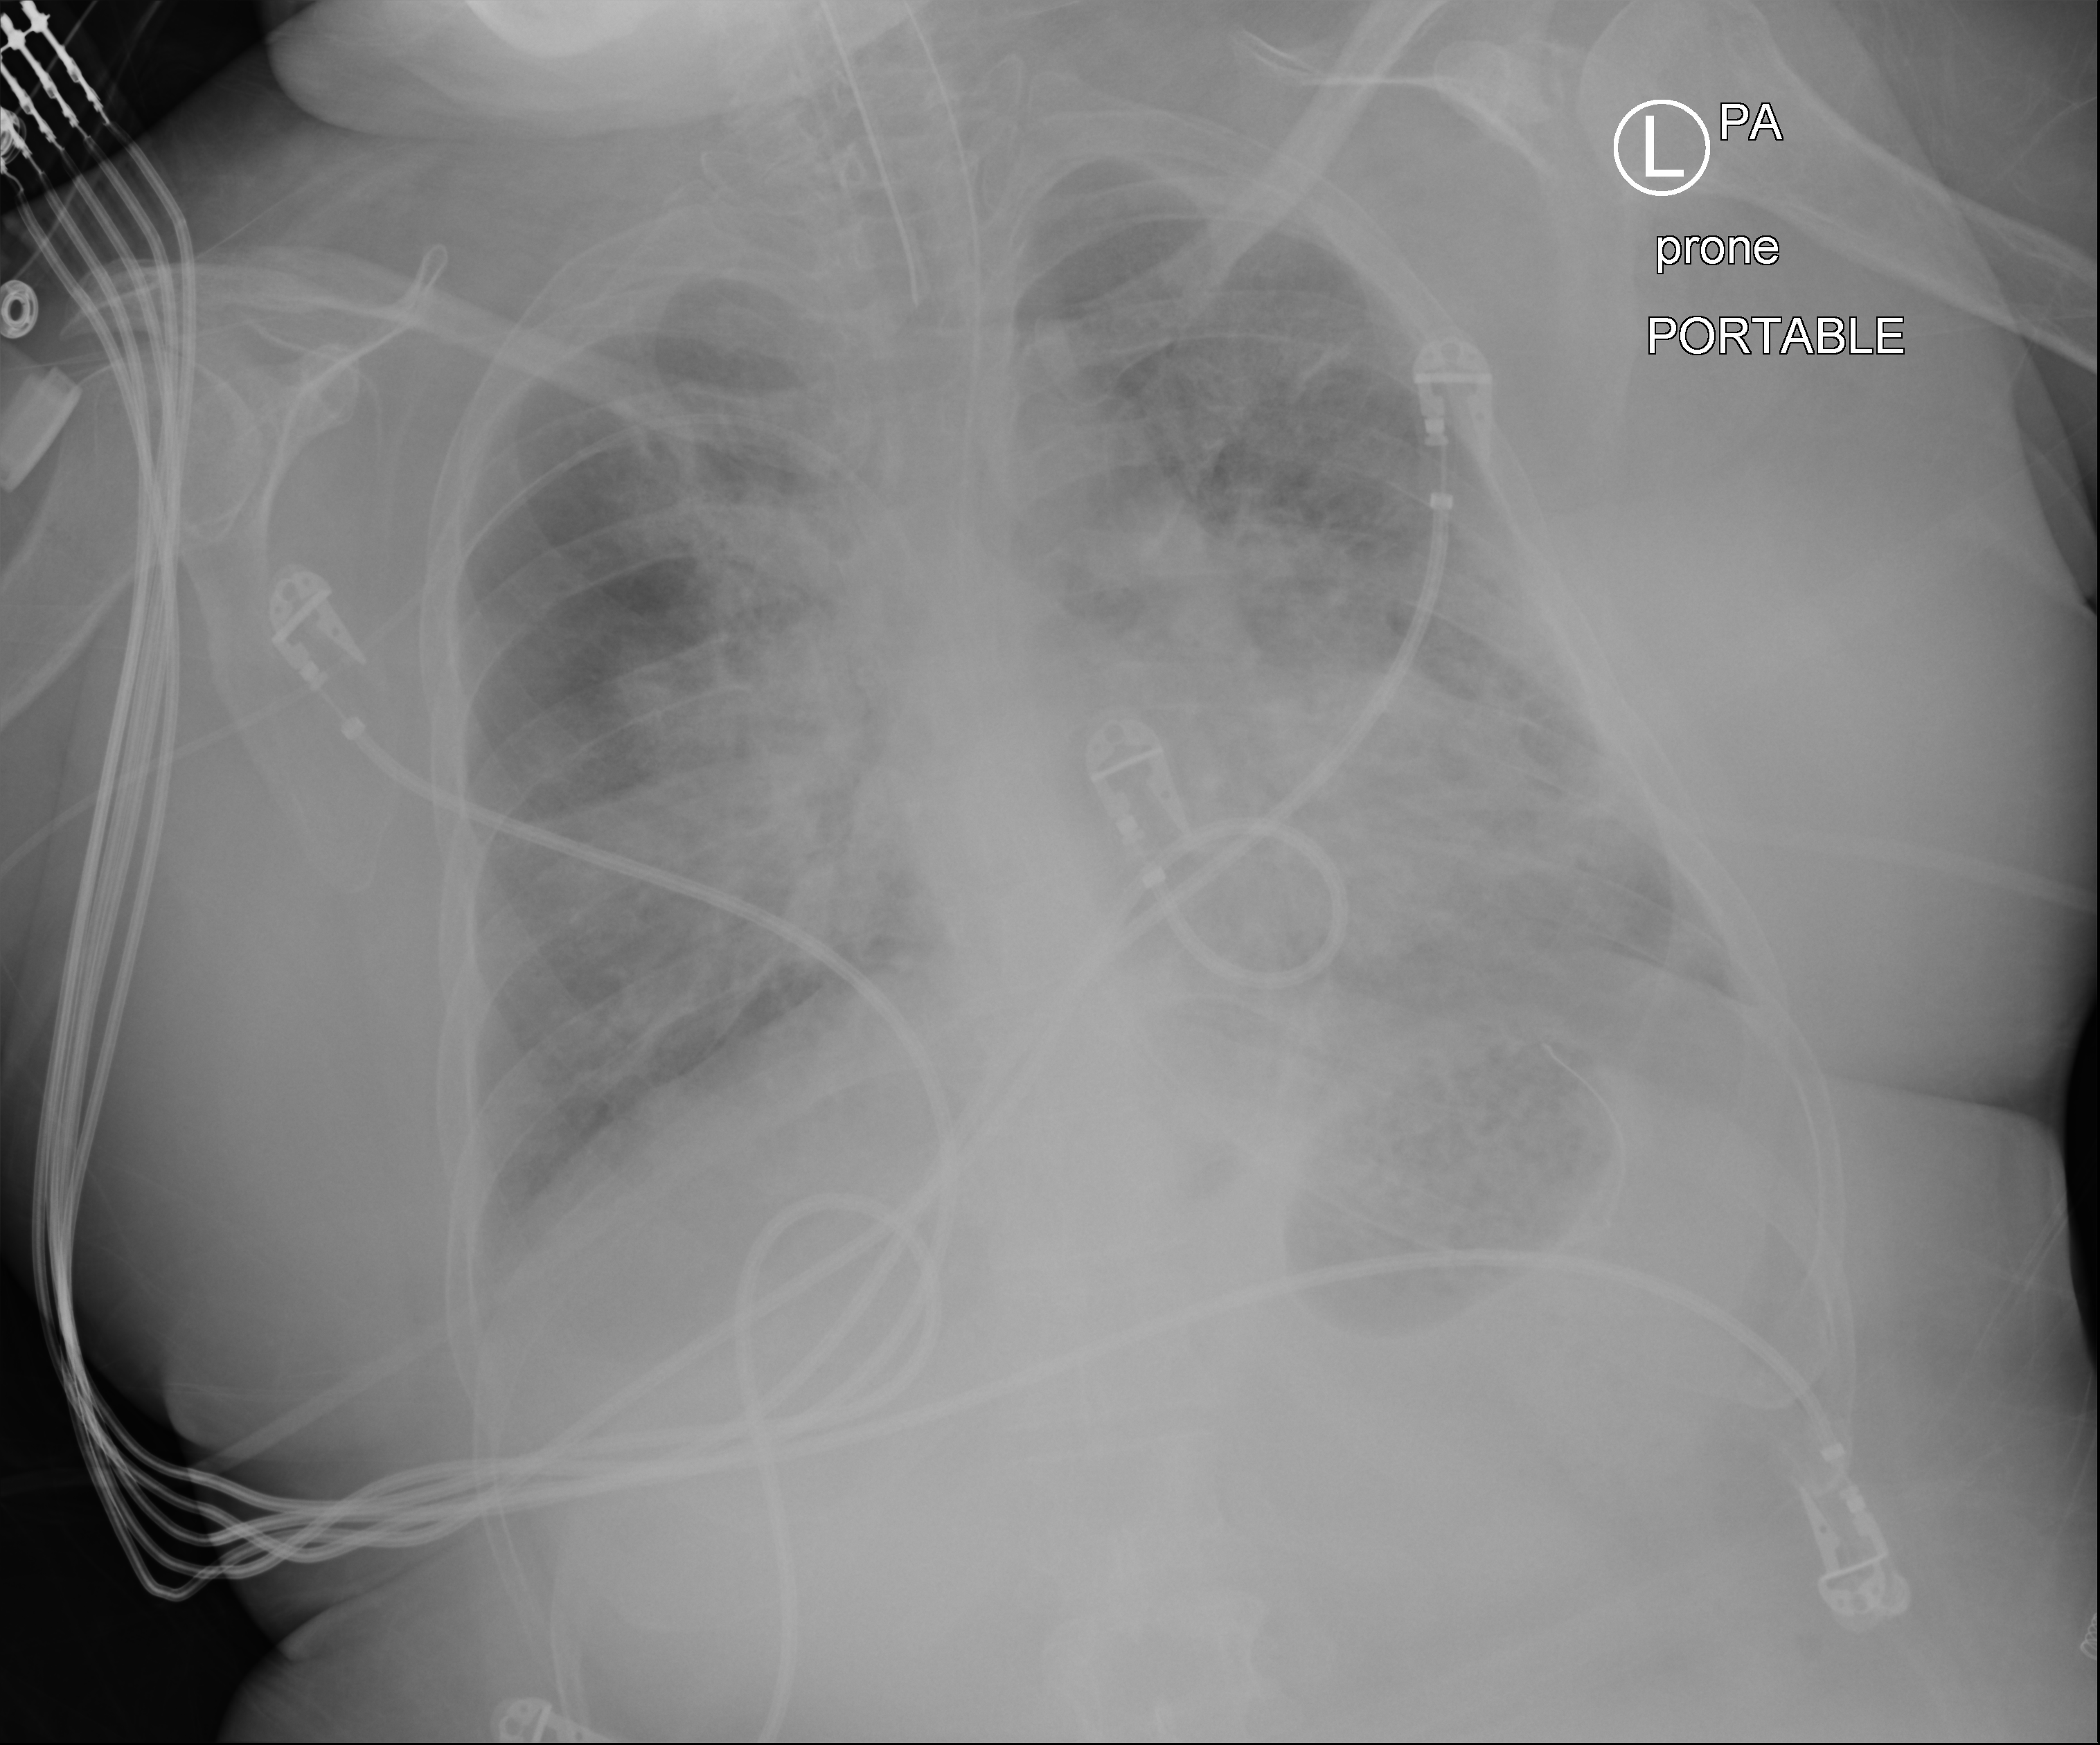
Chest radiograph (computed radiography), posteroanterior (PA) projection. Patient hospitalised with COVID-19, aged 18–59 years.
From the hospital-stay record, not from the radiograph (when in the stay this image was taken is not recorded):
- length of hospital stay: 15 days
- admitted to intensive care during this hospital stay: yes
- mechanically ventilated during this hospital stay: yes